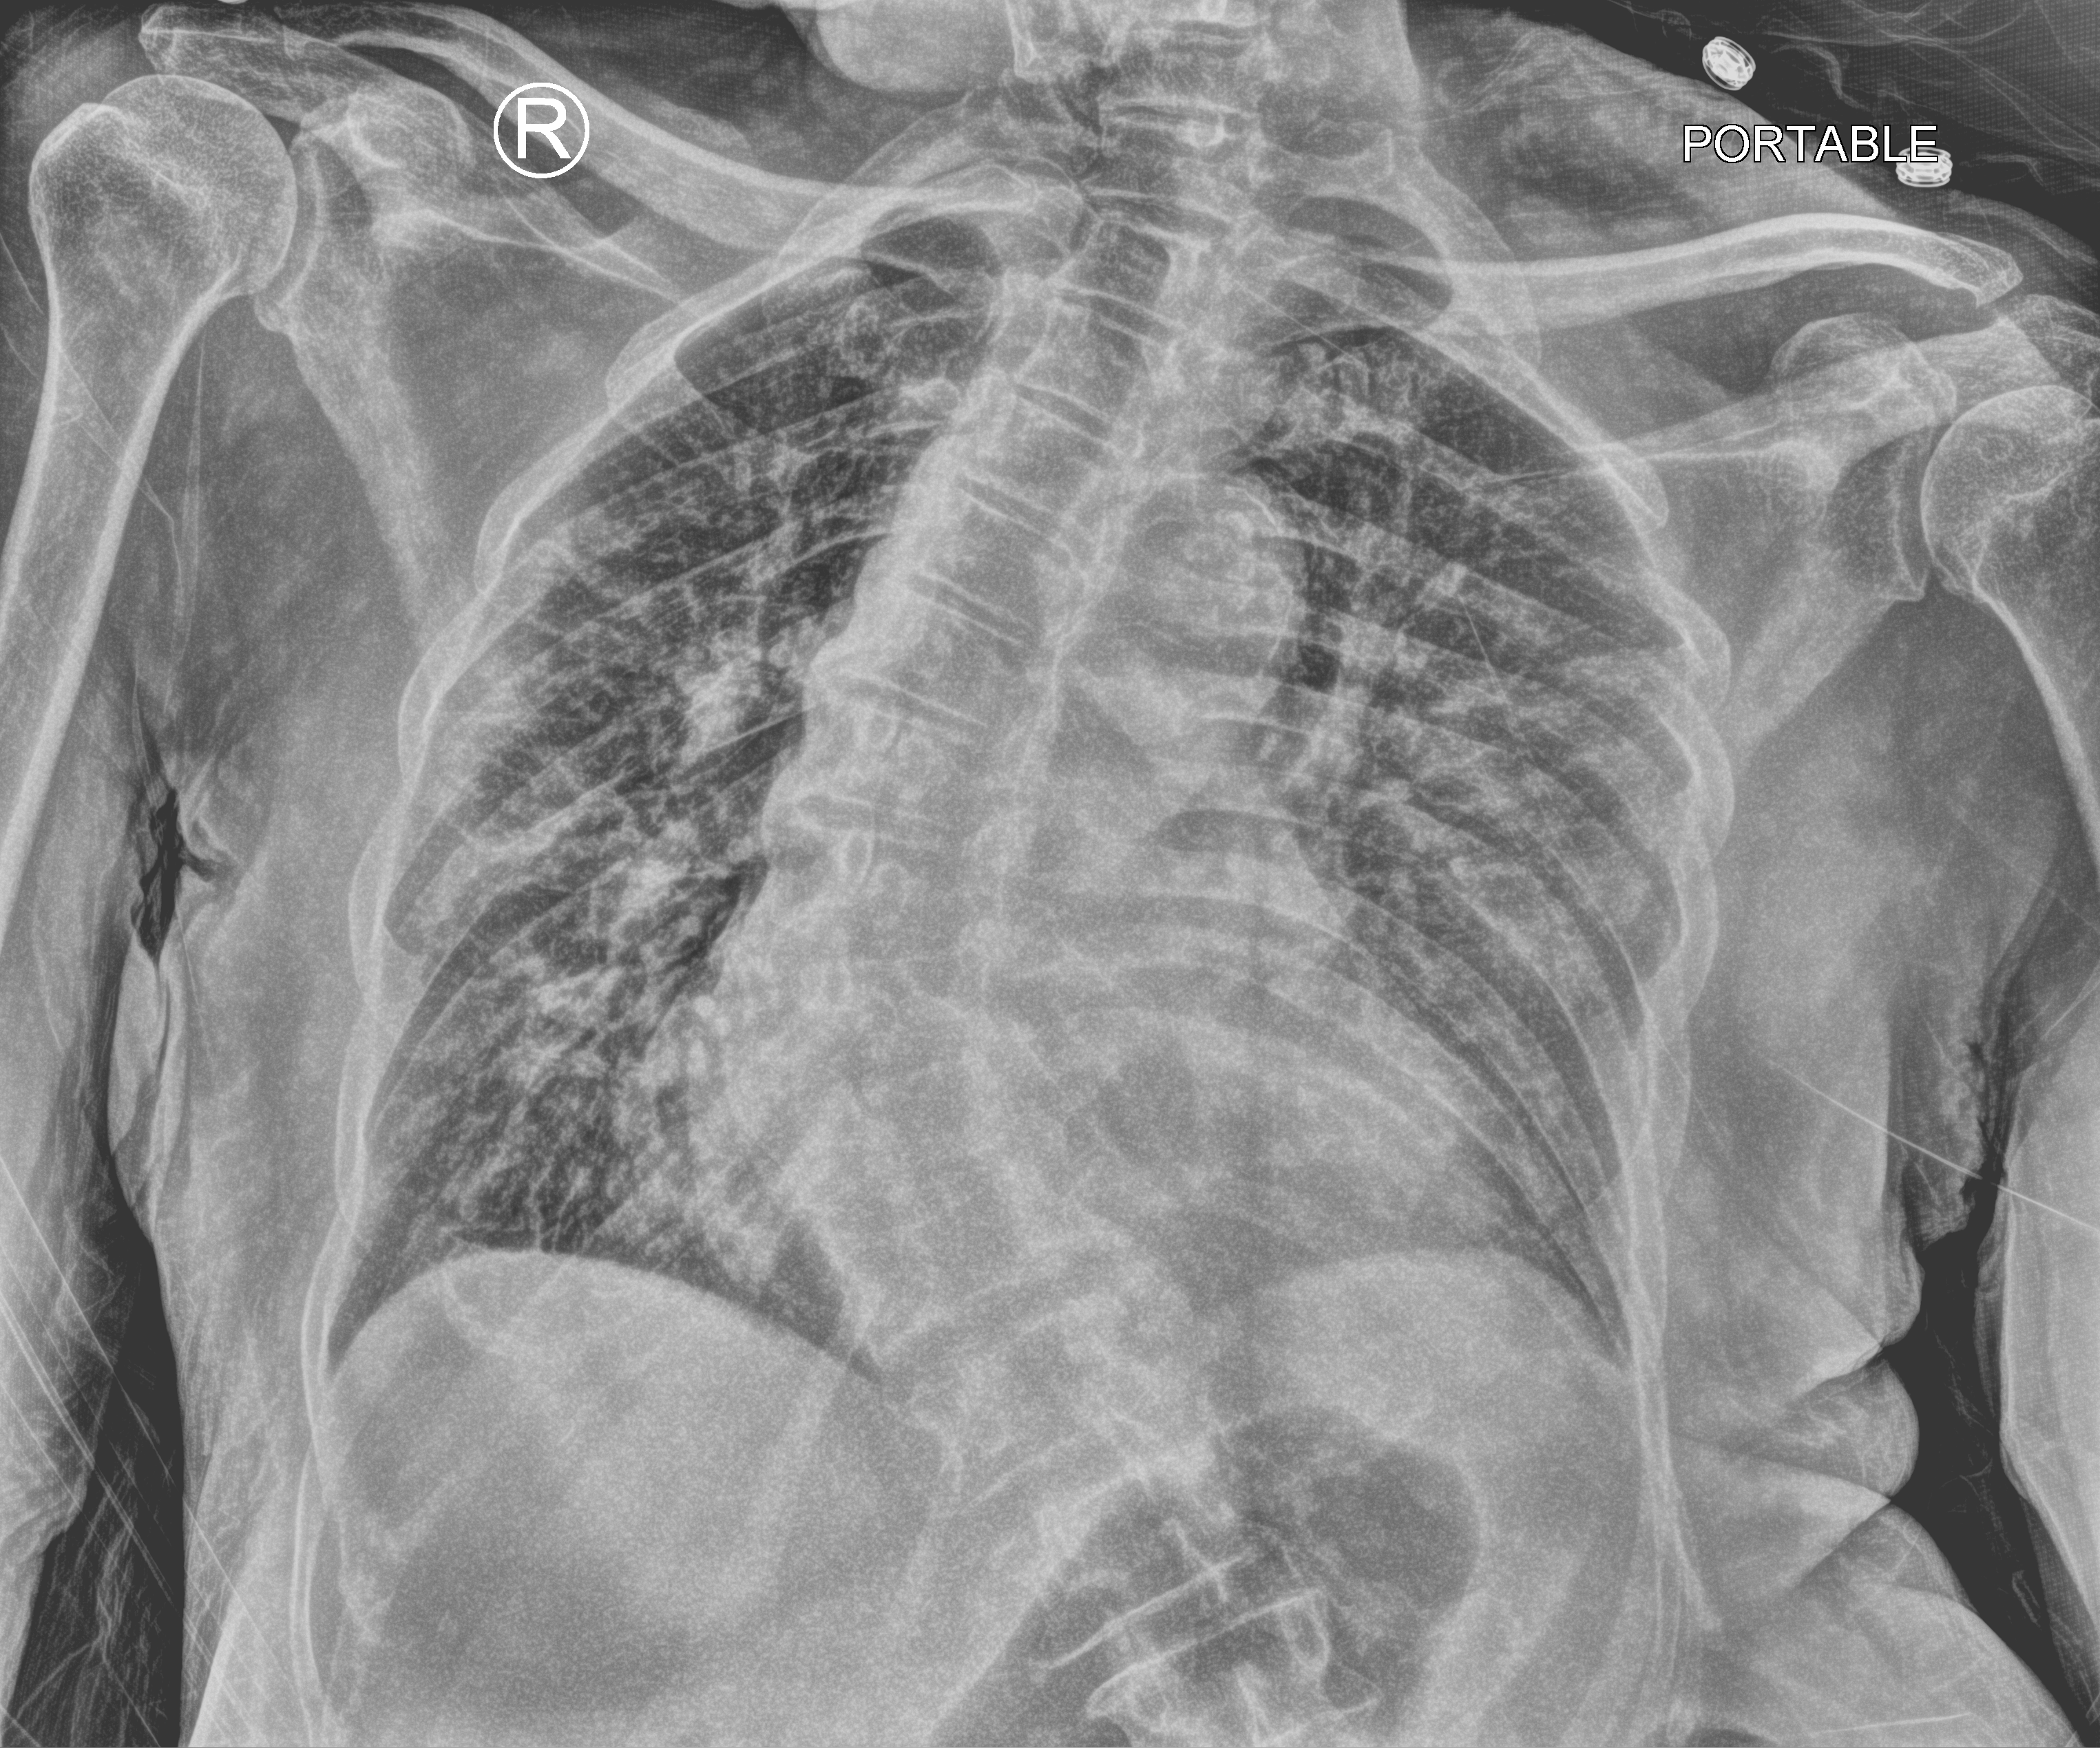
Chest X-ray (portable). Male patient hospitalised with COVID-19, age 75–90 years.
Hospital-stay facts (about this admission, not read from this image; timing relative to this image not recorded): admitted to intensive care during this hospital stay: no.